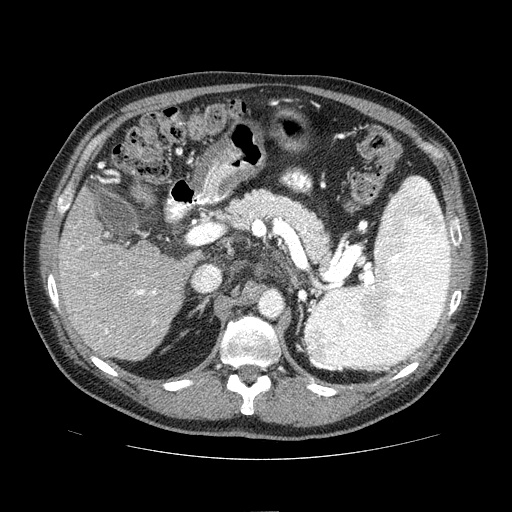
Contrast-enhanced abdominal CT (liver protocol), one axial slice. Position 37 of 81 along the scan axis. One of 2 acquisitions stored at this slice position. Soft-tissue window (W 400 / L 40 HU). 2.5 mm slice thickness. 512 × 512 image matrix, field of view 400 × 400 mm. Case-level facts recorded for this patient, not image findings: diagnosis: hepatocellular carcinoma (patient treated with transarterial chemoembolisation; whether this scan precedes or follows treatment is not stated here); TNM stage (as recorded): Stage-IIIA; Child-Pugh class: A; tumour differentiation: well differentiated; tumour nodularity: multinodular.
Structures marked on this image (semi-automatically segmented with operator editing):
- liver parenchyma outside the tumour (the mass and vessels are separate outlines, so this box may not span the whole liver): bounding box (x1, y1, x2, y2) in pixels: (58, 186, 196, 360)
- liver vessels: (66, 234, 157, 352)